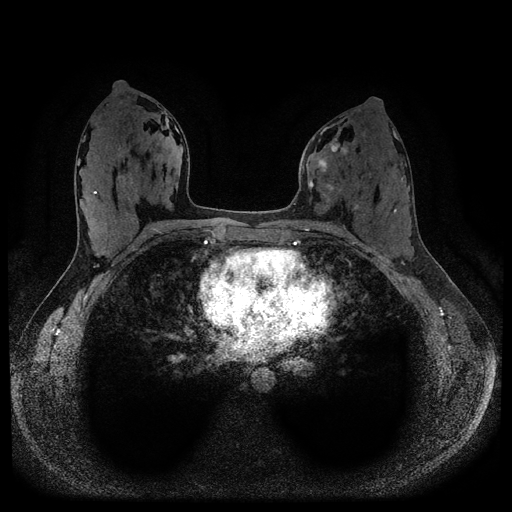
Breast MRI (dynamic contrast-enhanced, multi-phase), one axial slice. Position 50 of 116 along the scan axis. Dynamic contrast-enhanced series, time point 2 of 5 at this slice position (early post-contrast). 1.5 T. TE 2.6 ms, TR 5.3 ms. 512 × 512 image matrix, field of view 350 × 350 mm. Patient: female, 33 years.
Annotated regions visible in this slice (semi-automatic segmentation, software-assisted and operator-edited):
- breast lesion (labelled 'tumour' in the annotation; benign lesions carry a separate 'benign' label): bounding box (x1, y1, x2, y2) in pixels: (307, 140, 341, 194)